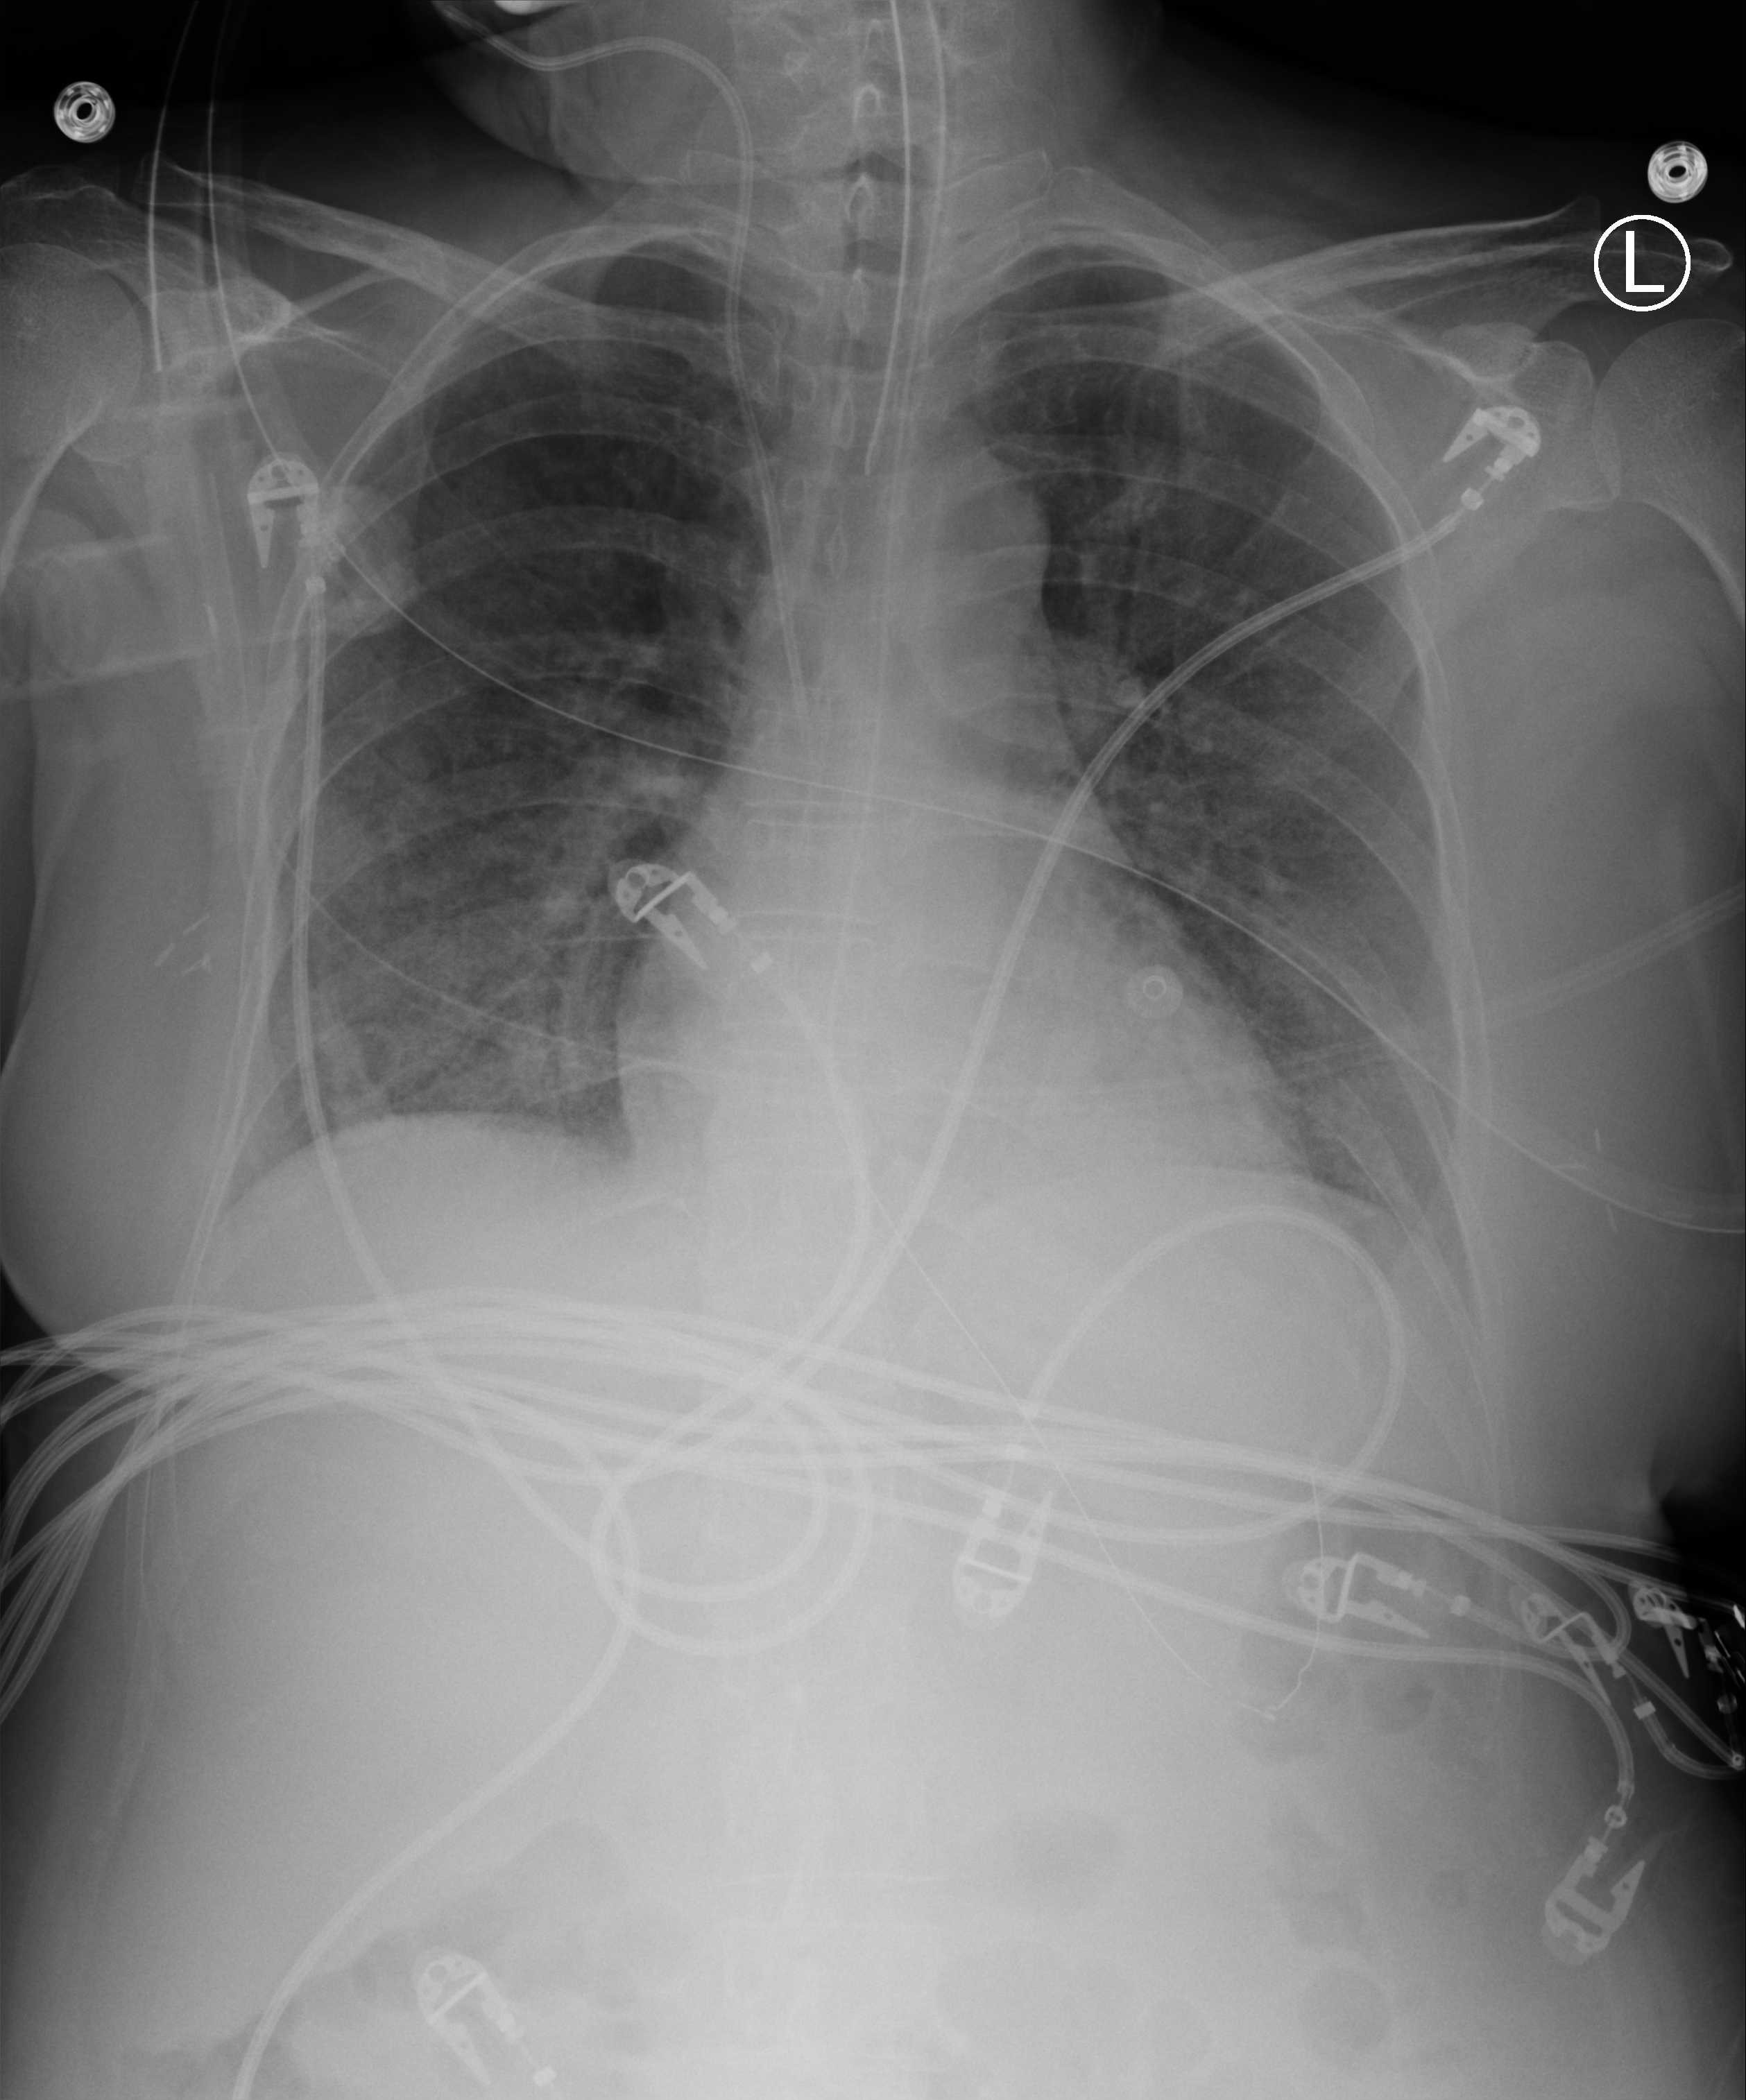
Chest X-ray (portable), anteroposterior (AP) projection. Patient hospitalised with COVID-19; female, aged 18–59 years.
Hospital-stay facts (about this admission, not read from this image; timing relative to this image not recorded): length of hospital stay: 21 days; mechanically ventilated during this hospital stay: yes; admitted to intensive care during this hospital stay: no.